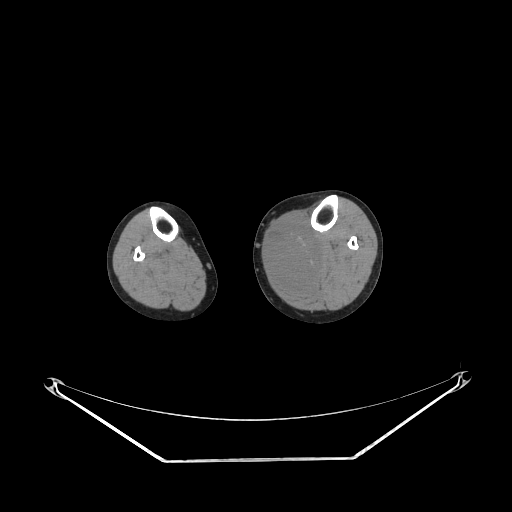
CT of an extremity soft-tissue mass (from a PET/CT study), one axial slice; slice 140 of 223 in the series (ordered by position); reconstruction kernel STANDARD; soft-tissue window (W 400 / L 40 HU); 3.75 mm slice thickness; 512 × 512 image matrix. Female patient. From the clinical record (not read from this slice): histological type: extraskeletal high grade osteogenic sarcoma; grade: high; site of the primary tumour: left calf.
Outlined on this slice (expert contour drawn on MRI and transferred to this co-registered scan by the dataset authors):
- gross tumour volume (mass): box from (x=269, y=224) to (x=320, y=289) px